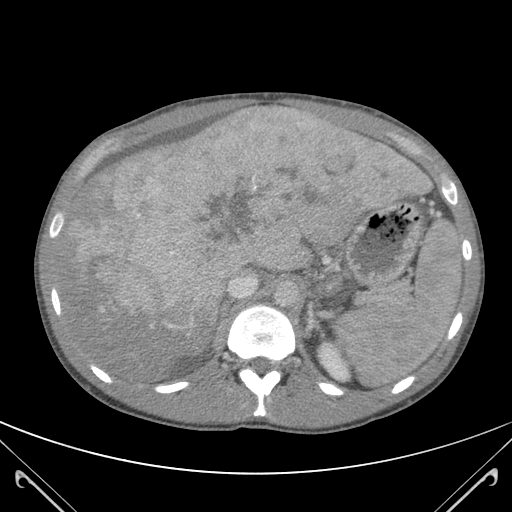
Contrast-enhanced abdominal CT (liver protocol), one axial slice. Position 81 of 118 along the scan axis. Soft-tissue window (W 400 / L 40 HU). 3 mm slice thickness. 512 × 512 image matrix, field of view 380 × 380 mm. Case-level facts recorded for this patient, not image findings: diagnosis: hepatocellular carcinoma (patient treated with transarterial chemoembolisation; whether this scan precedes or follows treatment is not stated here); TNM stage (as recorded): Stage-IIIB; Child-Pugh class: A.
Outlined on this slice (semi-automatic segmentation, software-assisted and operator-edited):
- abdominal aorta: bounding box <273,283,298,308> (left, top, right, bottom; pixels)
- liver parenchyma outside the tumour (the mass and vessels are separate outlines, so this box may not span the whole liver): <59,111,423,378>
- mass: <87,115,418,336>
- liver vessels: <79,113,301,312>